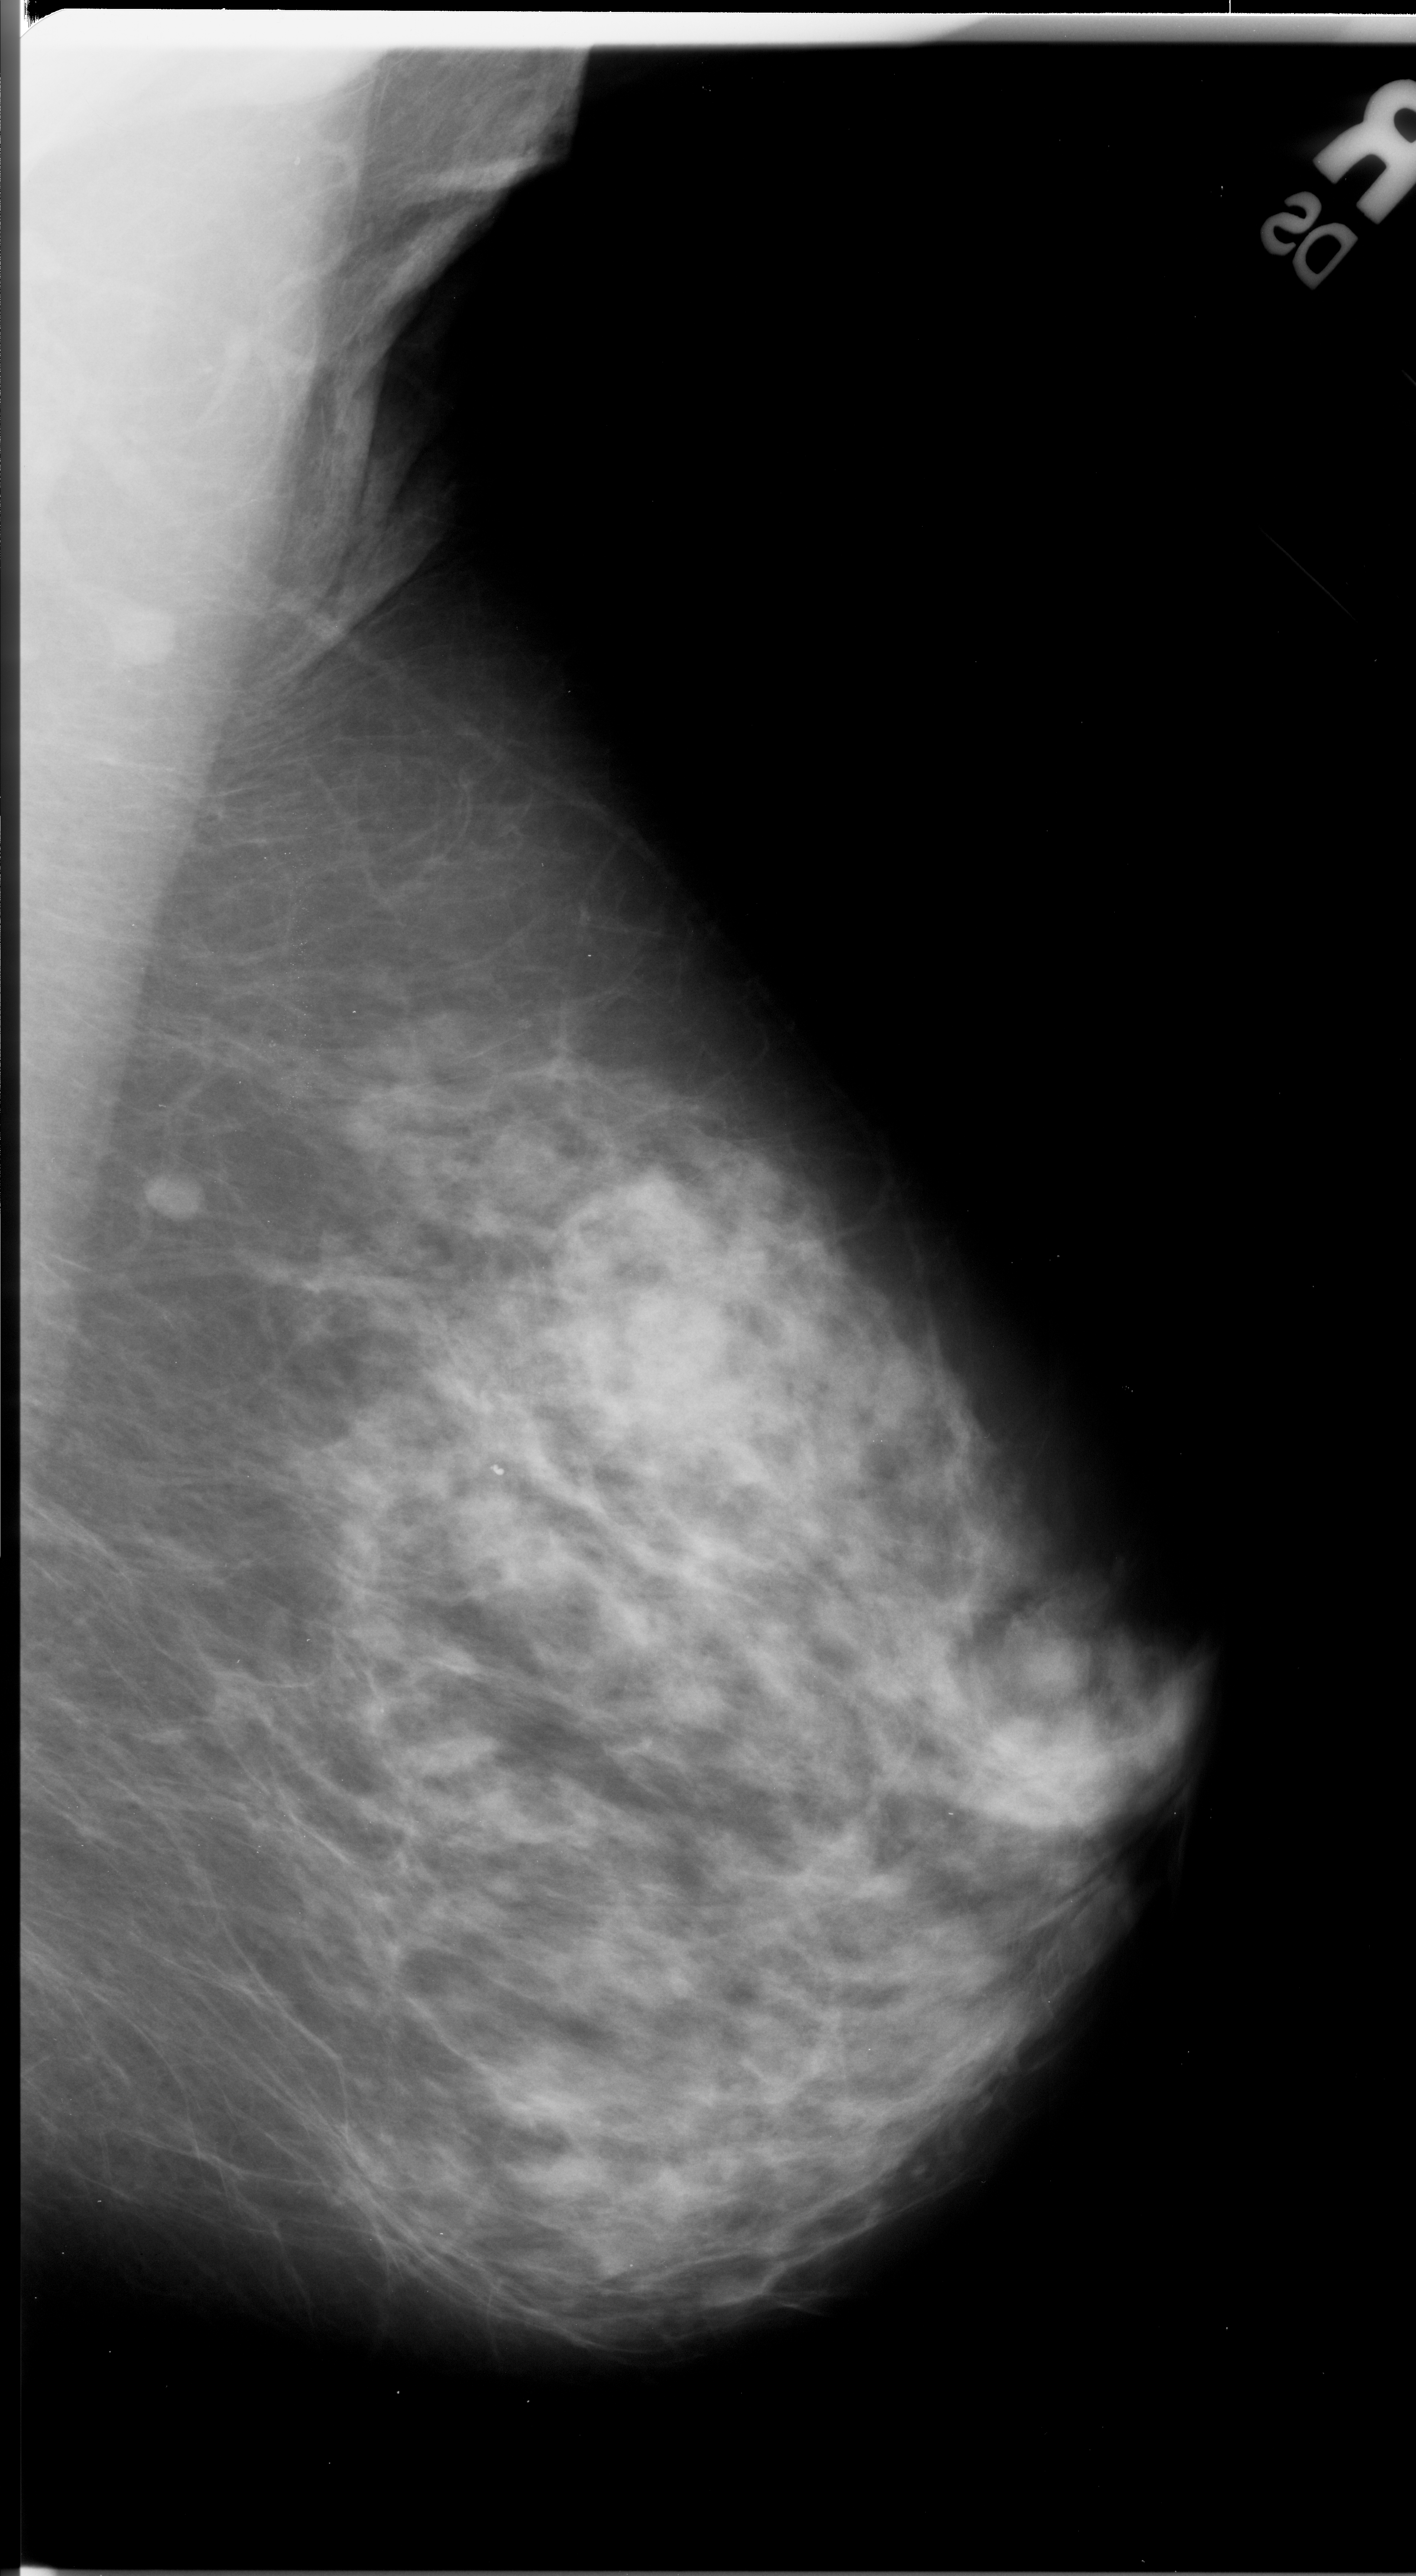
Digitized screen-film mammogram; right breast; MLO view; 1416 × 2576 image matrix.
Expert-marked regions of interest on this film, with their recorded descriptors:
- mass, shape architectural distortion, margins spiculated; BI-RADS assessment category 5; subtlety rating 1 on a 1 (subtle) to 5 (obvious) scale; pathology (as recorded): malignant: bounding box <284,1407,417,1564> (left, top, right, bottom; pixels)